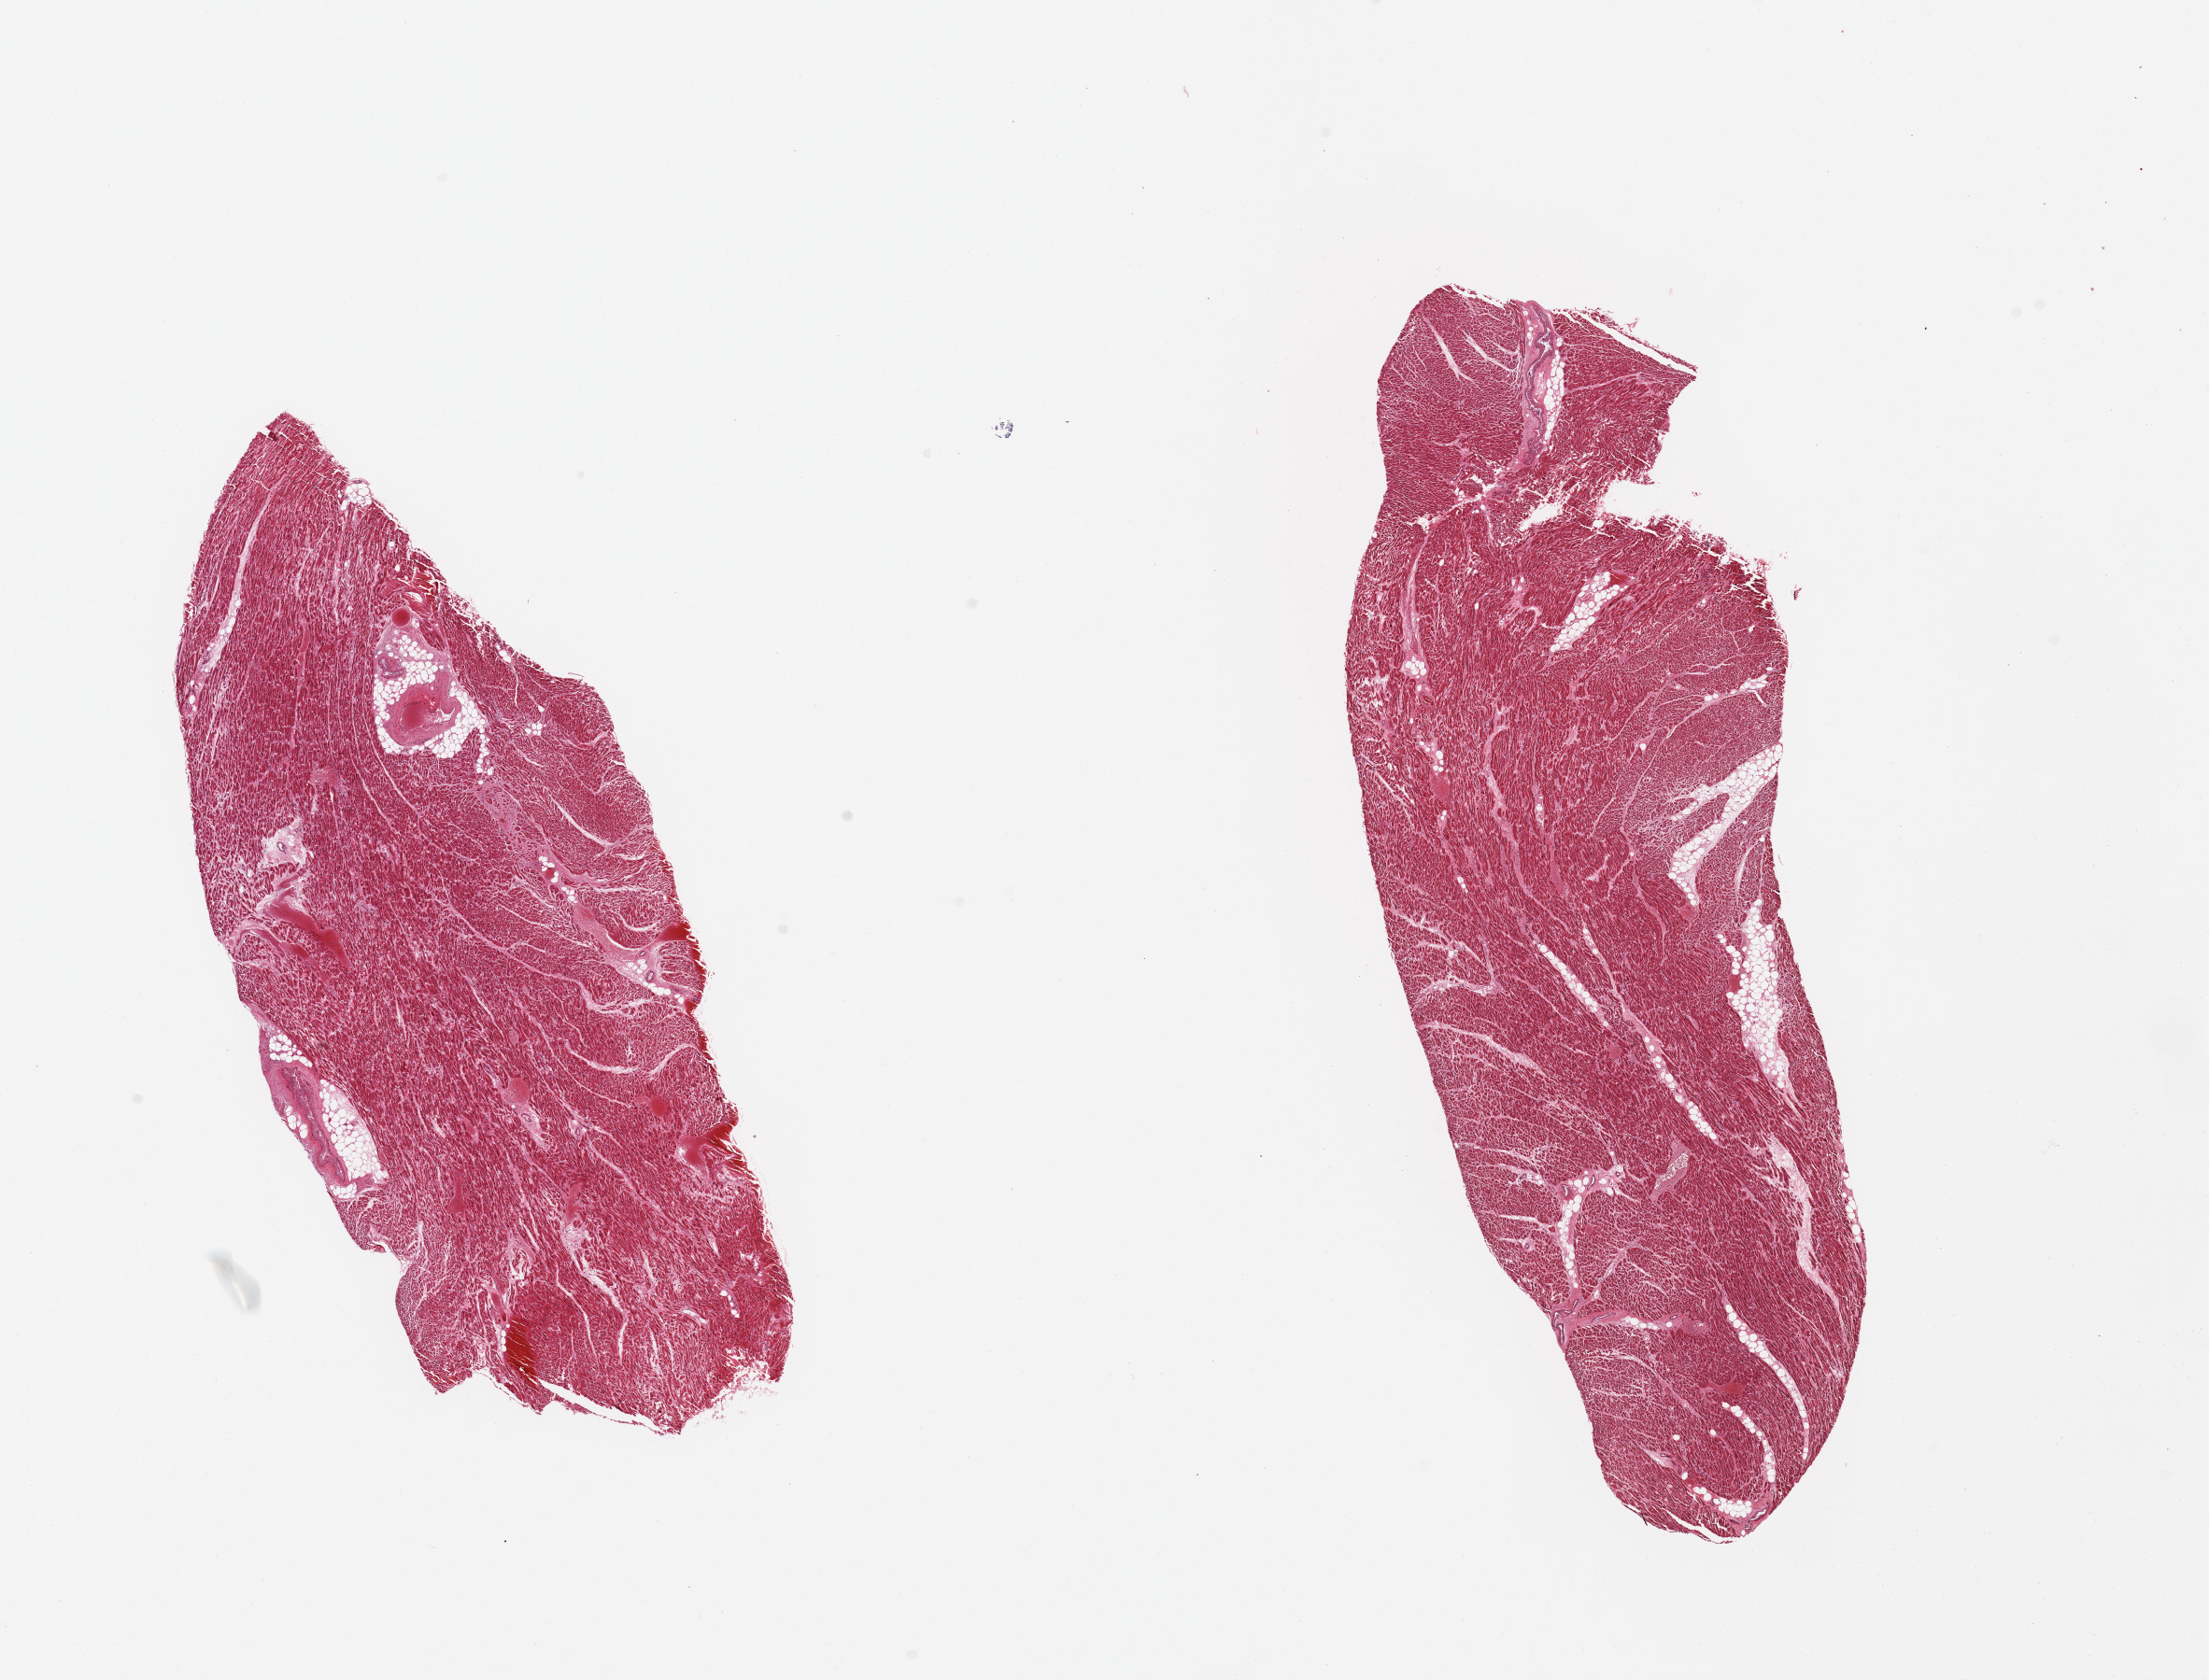
H&E whole-slide image, brightfield, shown as a low-resolution overview of the whole scanned area (about 18.7 x 14.2 mm). PAXgene-fixed, paraffin-embedded tissue. Section of heart (target tissue). Donor tissue sample. Donor: male.
Review note (as recorded): 2 pieces; 5% internal fat.